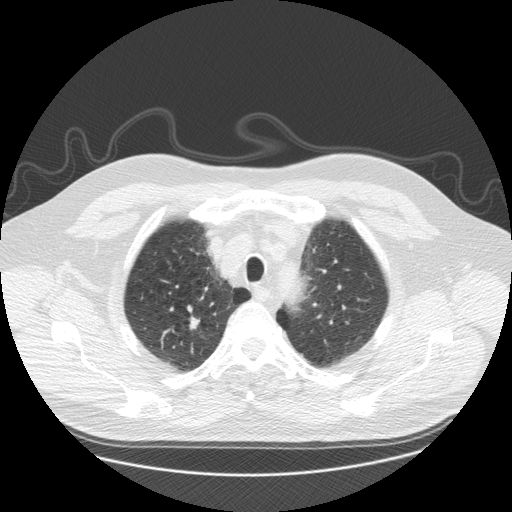
Chest CT (low-dose screening protocol), one axial image; third screening round (two years after baseline); lung window (W 1500 / L -600 HU); 2.5 mm slice thickness; 120 kVp; slice 29 of 173 in the series. Male, age 61 years at enrolment. Former smoker at enrolment.
- Expert-annotated lung lesion, bounding box [x1, y1, x2, y2] px = [174, 305, 212, 339].
- Screening reader's record for this exam (one nodule recorded; not confirmed to be the boxed lesion): non-calcified nodule or mass ≥4 mm, right upper lobe, 10 × 7 mm, smooth margins, soft tissue attenuation, pre-existing on the prior screen: yes; interval growth: yes.
- Participant outcome: lung cancer diagnosed 110 days after this screen — squamous cell carcinoma, NOS, right upper lobe, moderately differentiated (G2), stage IA (AJCC 6th edition), 10 mm at pathology.